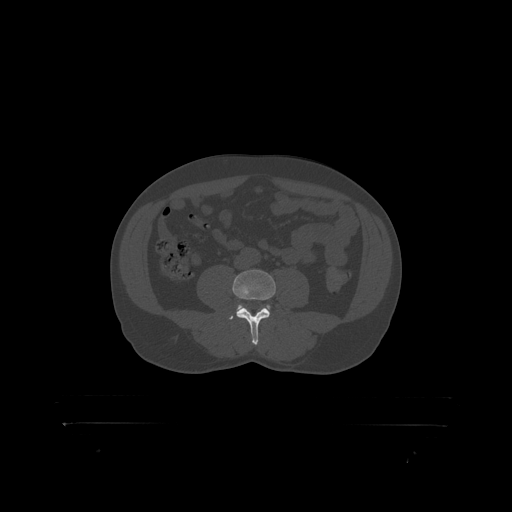
CT including the spine, one axial slice. 120 kVp. Bone window (W 1800 / L 400 HU). 512 × 512 image matrix. Male patient, age 46 years. From the clinical record (not read from this slice): primary cancer: skin.
Annotated regions visible in this slice (semi-automatically segmented with operator editing):
- L4 vertebra: box from (x=233, y=270) to (x=276, y=319) px
- L5 vertebra: (x=237, y=305)–(x=271, y=310)